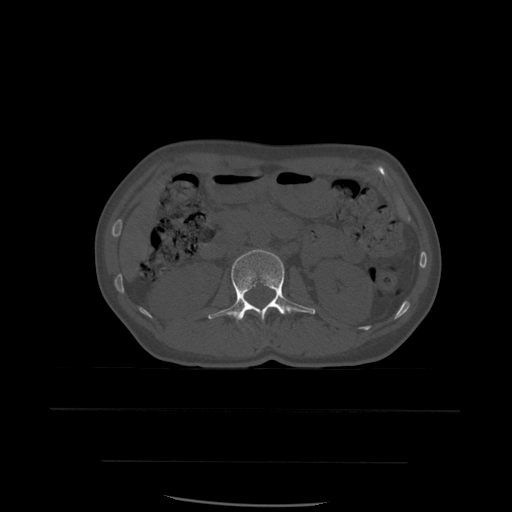
CT including the spine, one axial slice; slice 227 of 574 in the series (ordered by position); bone window (W 1800 / L 400 HU); 1.25 mm slice thickness; 512 × 512 image matrix. Patient age 48 years. From the clinical record (not read from this slice): primary cancer: lung.
Annotated regions visible in this slice (semi-automatically segmented with operator editing):
- L2 vertebra: bounding box (x1, y1, x2, y2) in pixels: (208, 250, 316, 325)